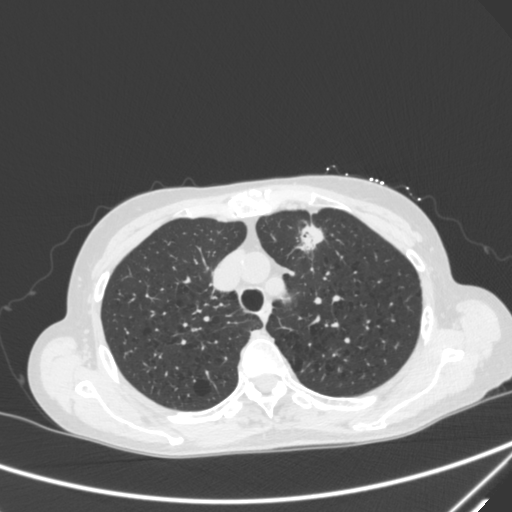
Chest CT, one axial slice; position 231 of 300 along the scan axis; 120 kVp; lung window (W 1500 / L -600 HU); 1 mm slice thickness; 512 × 512 image matrix, field of view 350 × 350 mm. Female patient, age 71 years. Case-level facts recorded for this patient, not image findings: clinical TNM (as recorded): T1c N0 M0; histopathological grade: G2-3.
Outlined on this slice (rectangle marked by the reading radiologist):
- lung tumour (recorded histology: adenocarcinoma): bounding box [x1, y1, x2, y2] px = [289, 218, 328, 268]